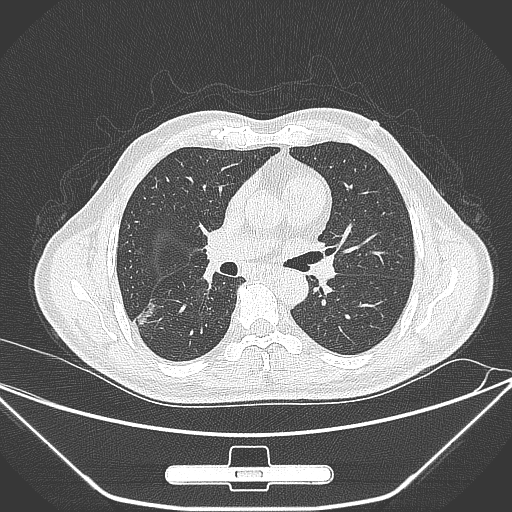
Chest CT, one axial slice. Slice 157 of 309 in the series (ordered by position). 120 kVp. Lung window (W 1500 / L -600 HU). 1 mm slice thickness. 512 × 512 image matrix. Patient: male, 71 years. Case-level facts recorded for this patient, not image findings: clinical TNM (as recorded): T1c N0 M0.
Annotated regions visible in this slice (bounding box drawn by a radiologist):
- lung tumour (recorded histology: adenocarcinoma): bounding box <131,298,161,331> (left, top, right, bottom; pixels)